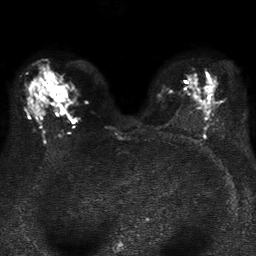
Breast MRI, one axial slice. Slice 21 of 37 in the series (ordered by position). Diffusion-weighted series; image 2 of 4 stored at this slice position (different b-values; order by instance number). 1.5 T. 256 × 256 image matrix. Female patient.
Structures marked on this image (expert manual segmentation):
- tumour on diffusion-weighted imaging: bounding box (x1, y1, x2, y2) in pixels: (52, 86, 66, 102)